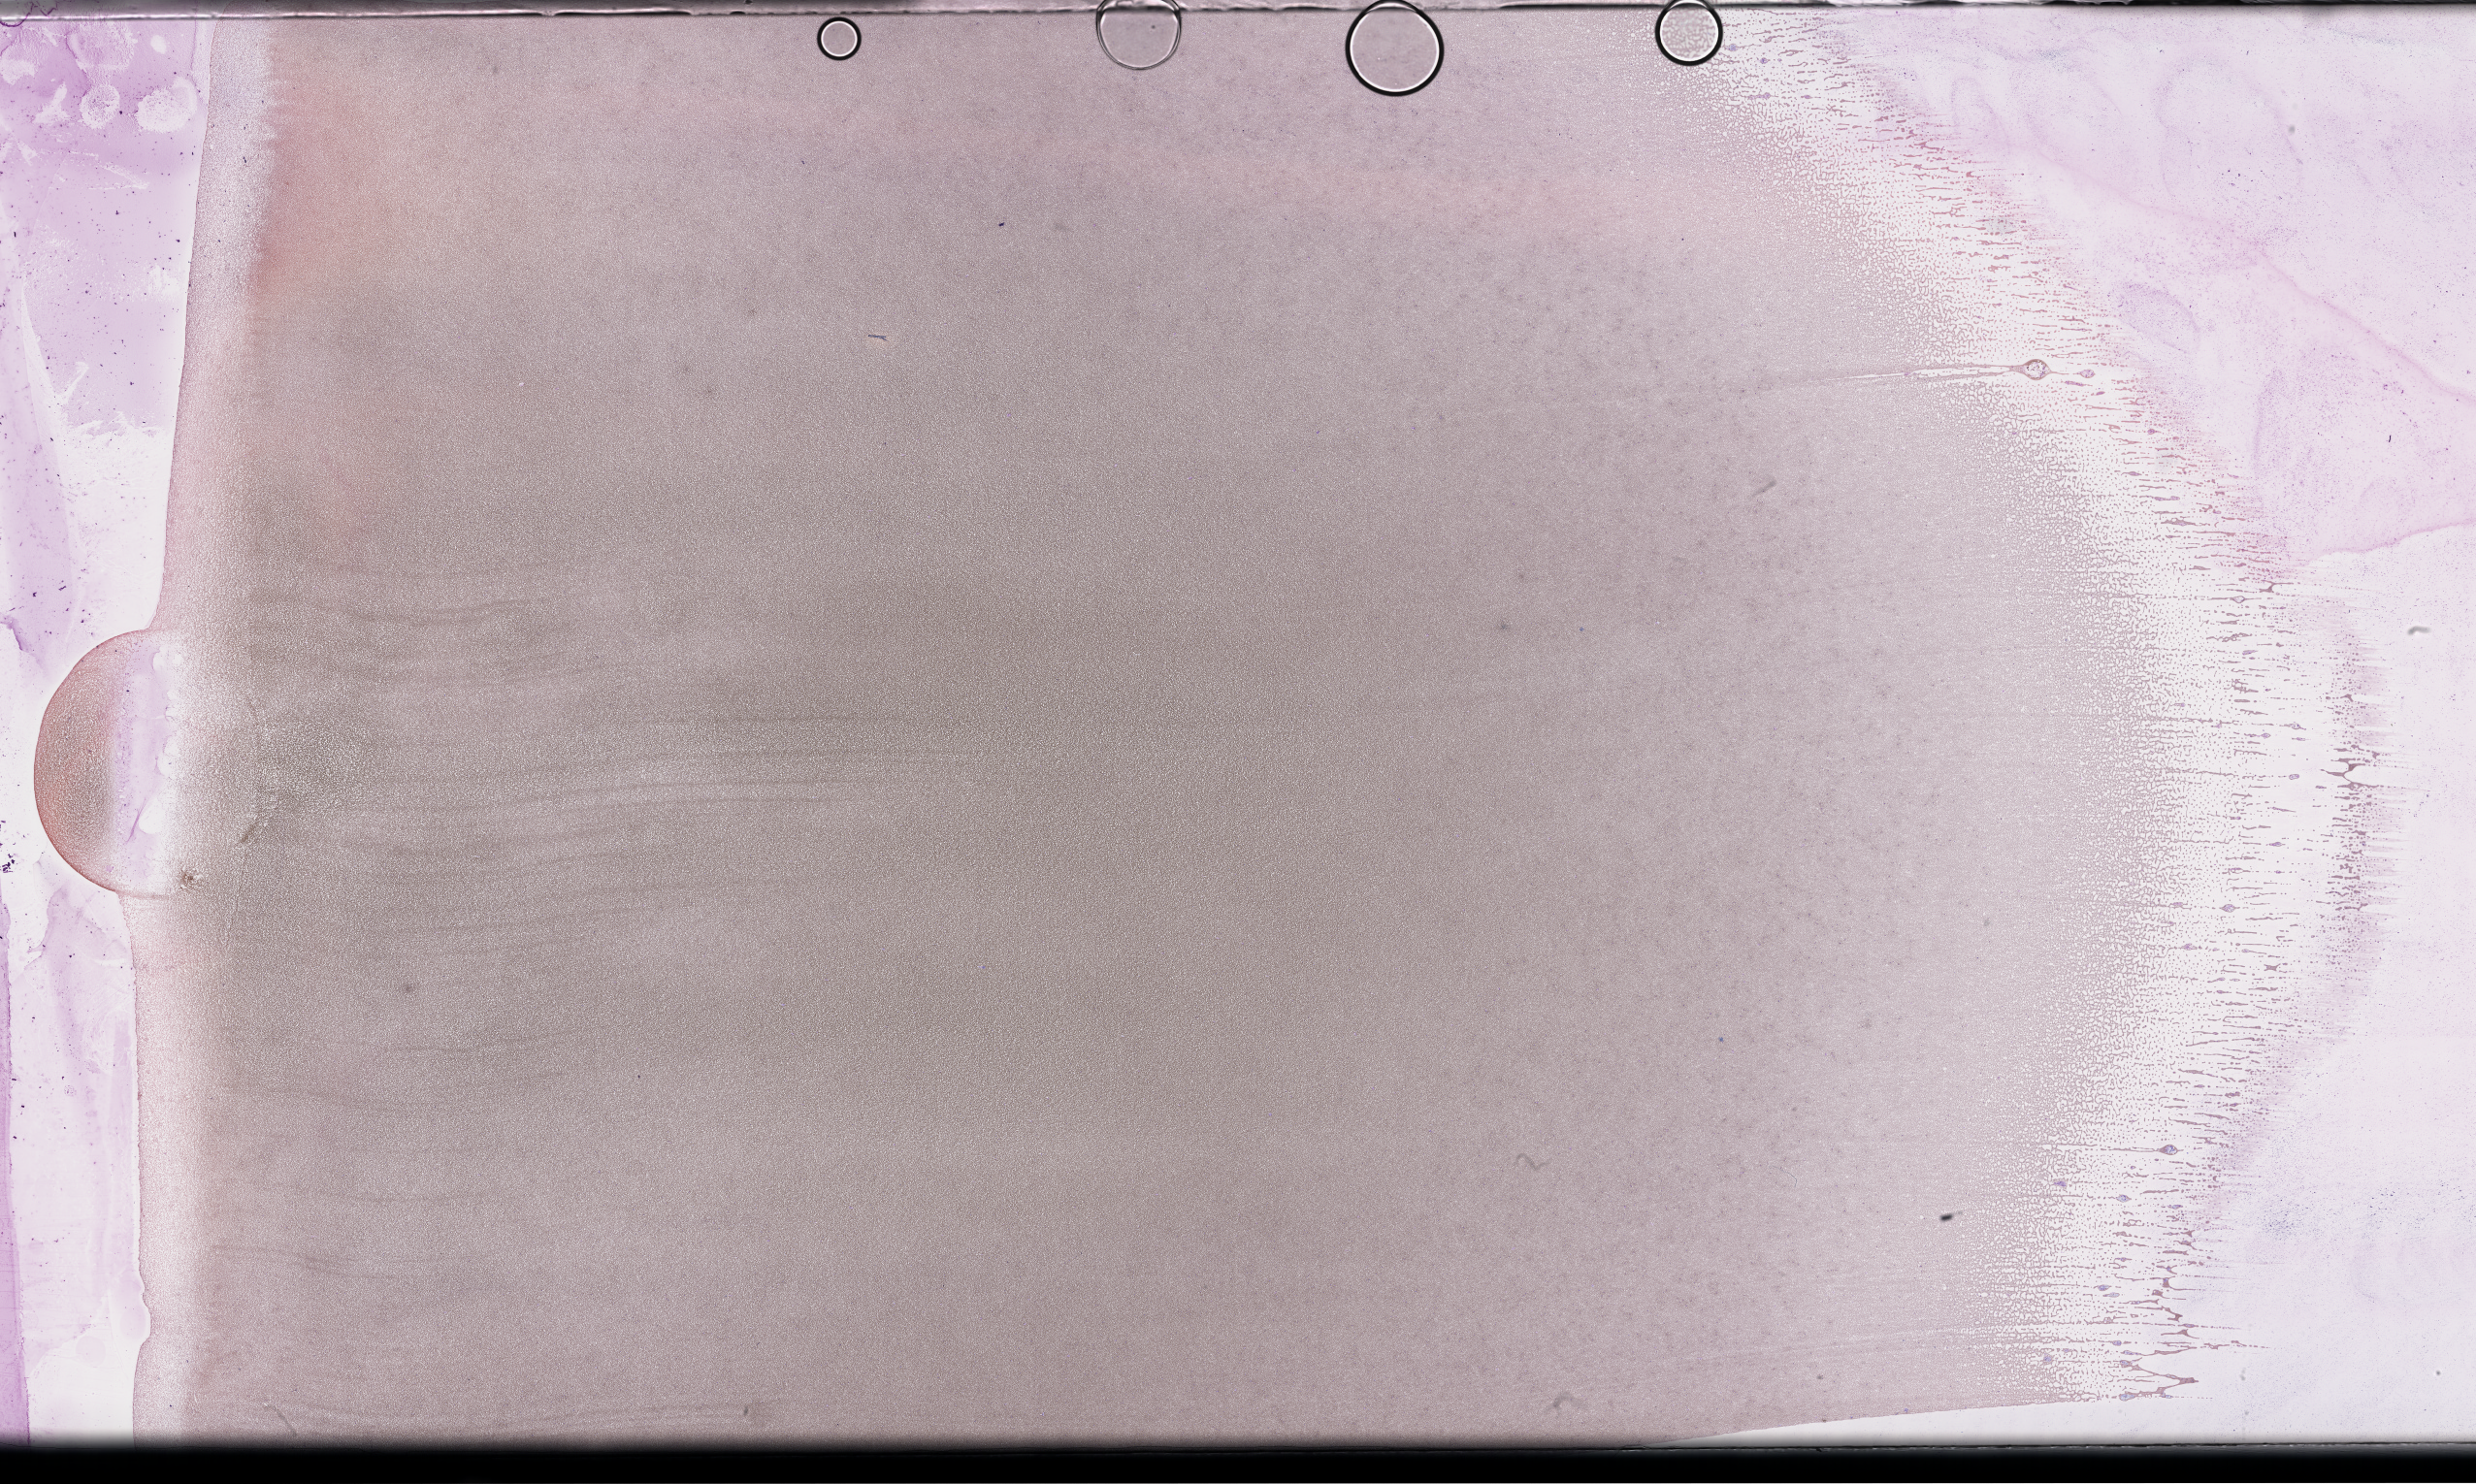
Wright–Giemsa-stained whole blood smear, whole-slide image — shown as a low-resolution overview of the whole scanned area (about 41.2 x 24.7 mm), collected on treatment. Patient sex: male.
* patient diagnosis: Plasma Cell Myeloma